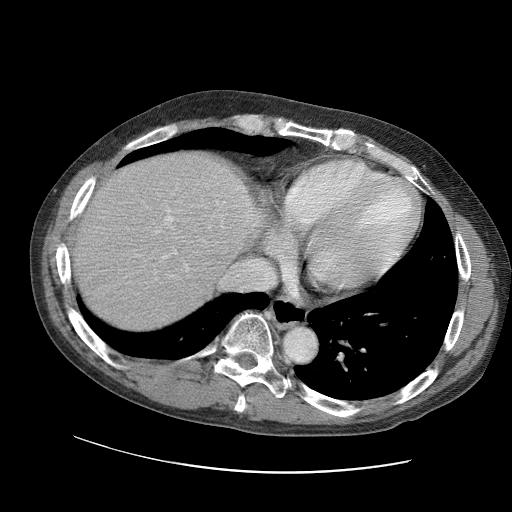
Contrast-enhanced abdominal CT (liver protocol), one axial slice. Reconstruction kernel STANDARD. Soft-tissue window (W 400 / L 40 HU). 512 × 512 image matrix, field of view 400 × 400 mm. From the clinical record (not read from this slice): diagnosis: hepatocellular carcinoma (patient treated with transarterial chemoembolisation; whether this scan precedes or follows treatment is not stated here); TNM stage (as recorded): Stage-IIIC; Child-Pugh class: B.
Annotated regions visible in this slice (semi-automatically segmented with operator editing):
- liver parenchyma outside the tumour (the mass and vessels are separate outlines, so this box may not span the whole liver): bounding box <68,150,262,330> (left, top, right, bottom; pixels)
- liver vessels: <140,191,224,281>